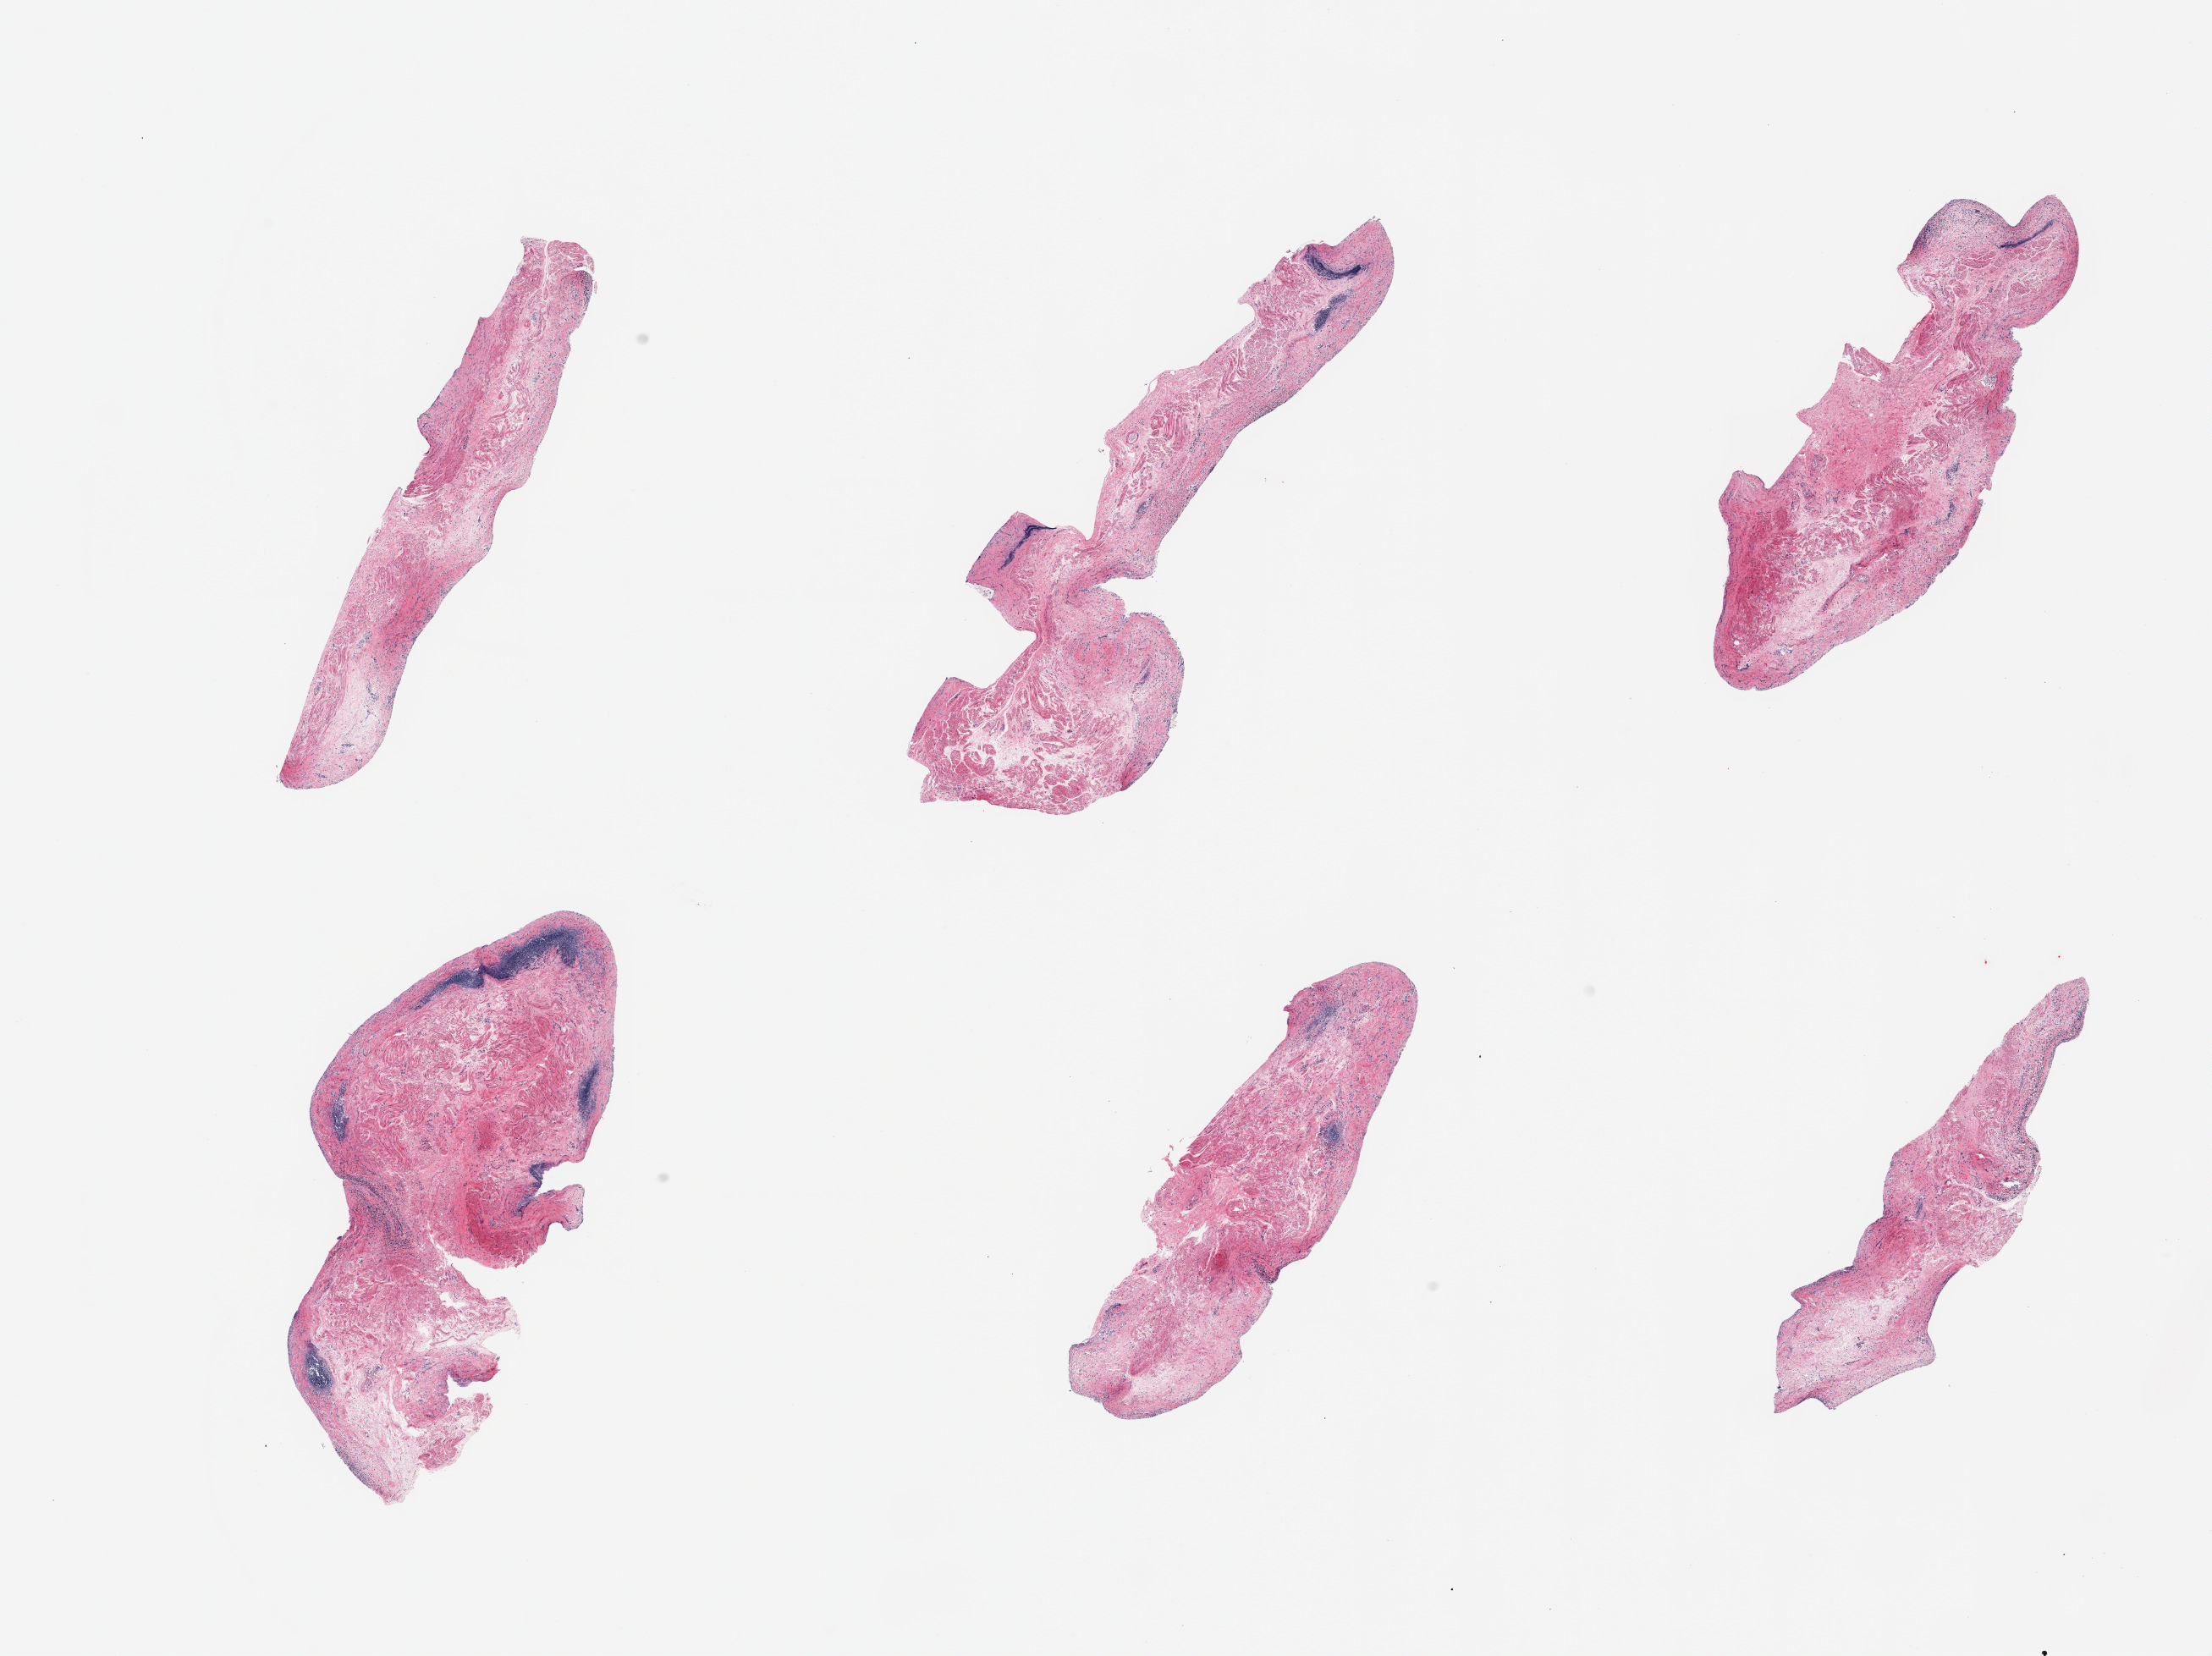
Haematoxylin and eosin whole-slide image, low-resolution overview of the scanned area, about 20.7 x 15.5 mm; PAXgene-fixed, paraffin-embedded tissue; target tissue: esophageal mucous membrane; tissue donor sample. Donor sex: male.
Pathologist's review note for this sample: 6 pieces, mucosa completely sloughed, unusually advanced autolysis.